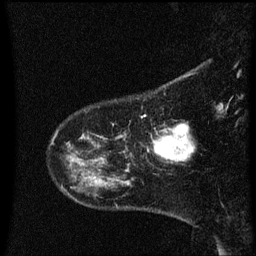
Breast MRI (dynamic contrast-enhanced), one sagittal slice. Position 9 of 60 along the scan axis. Dynamic contrast-enhanced series, image 2 of 3 at this slice position (ordered by acquisition). 1.5 T. TE 4.2 ms, TR 8.4 ms. 2 mm slice thickness. 256 × 256 image matrix, field of view 200 × 200 mm. Female patient, age 41 years. Case-level facts recorded for this patient, not image findings: setting: breast cancer imaged before/during neoadjuvant chemotherapy; receptor status: triple-negative.
Structures marked on this image (semi-automatic segmentation, software-assisted and operator-edited):
- analysis volume of interest (the breast-tissue region the enhancement analysis was run in; not a lesion): bounding box (x1, y1, x2, y2) in pixels: (147, 124, 191, 163)
- tumour enhancement mask (voxels above the 70 % enhancement threshold inside the analysis volume of interest): (155, 124, 190, 161)